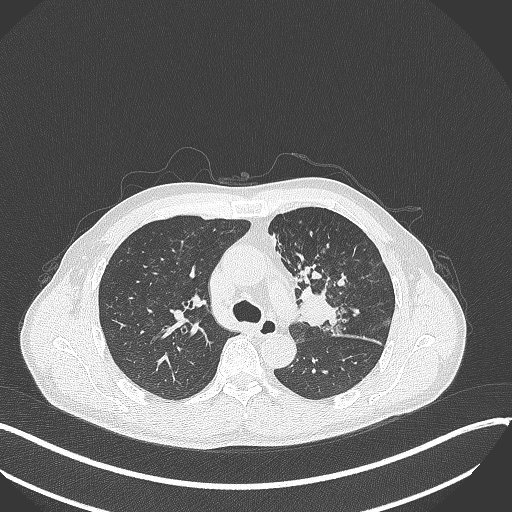
Chest CT, one axial slice; 120 kVp; lung window (W 1500 / L -600 HU); 512 × 512 image matrix, field of view 400 × 400 mm. Patient: male, 56 years. Case-level facts recorded for this patient, not image findings: clinical TNM (as recorded): T2a N0 M0.
Annotated regions visible in this slice (rectangle marked by the reading radiologist):
- lung tumour (recorded histology: squamous cell carcinoma): bounding box (x1, y1, x2, y2) in pixels: (293, 282, 343, 332)